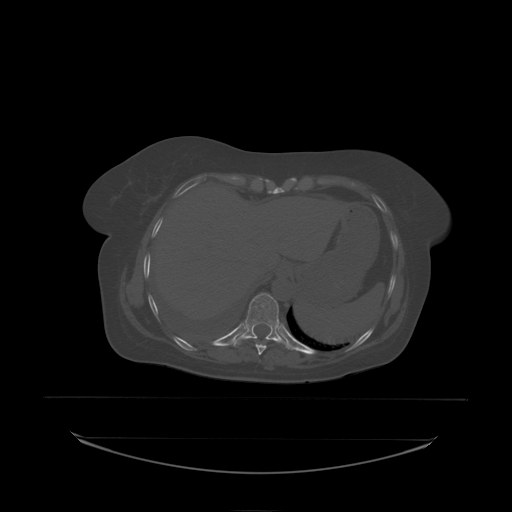
CT including the spine, one axial slice. Bone window (W 1800 / L 400 HU). 2.5 mm slice thickness. 512 × 512 image matrix. Patient: female, 53 years. Case-level facts recorded for this patient, not image findings: primary cancer: lung.
Outlined on this slice (semi-automatic segmentation, software-assisted and operator-edited):
- T10 vertebra: bounding box [x1, y1, x2, y2] px = [241, 294, 280, 338]